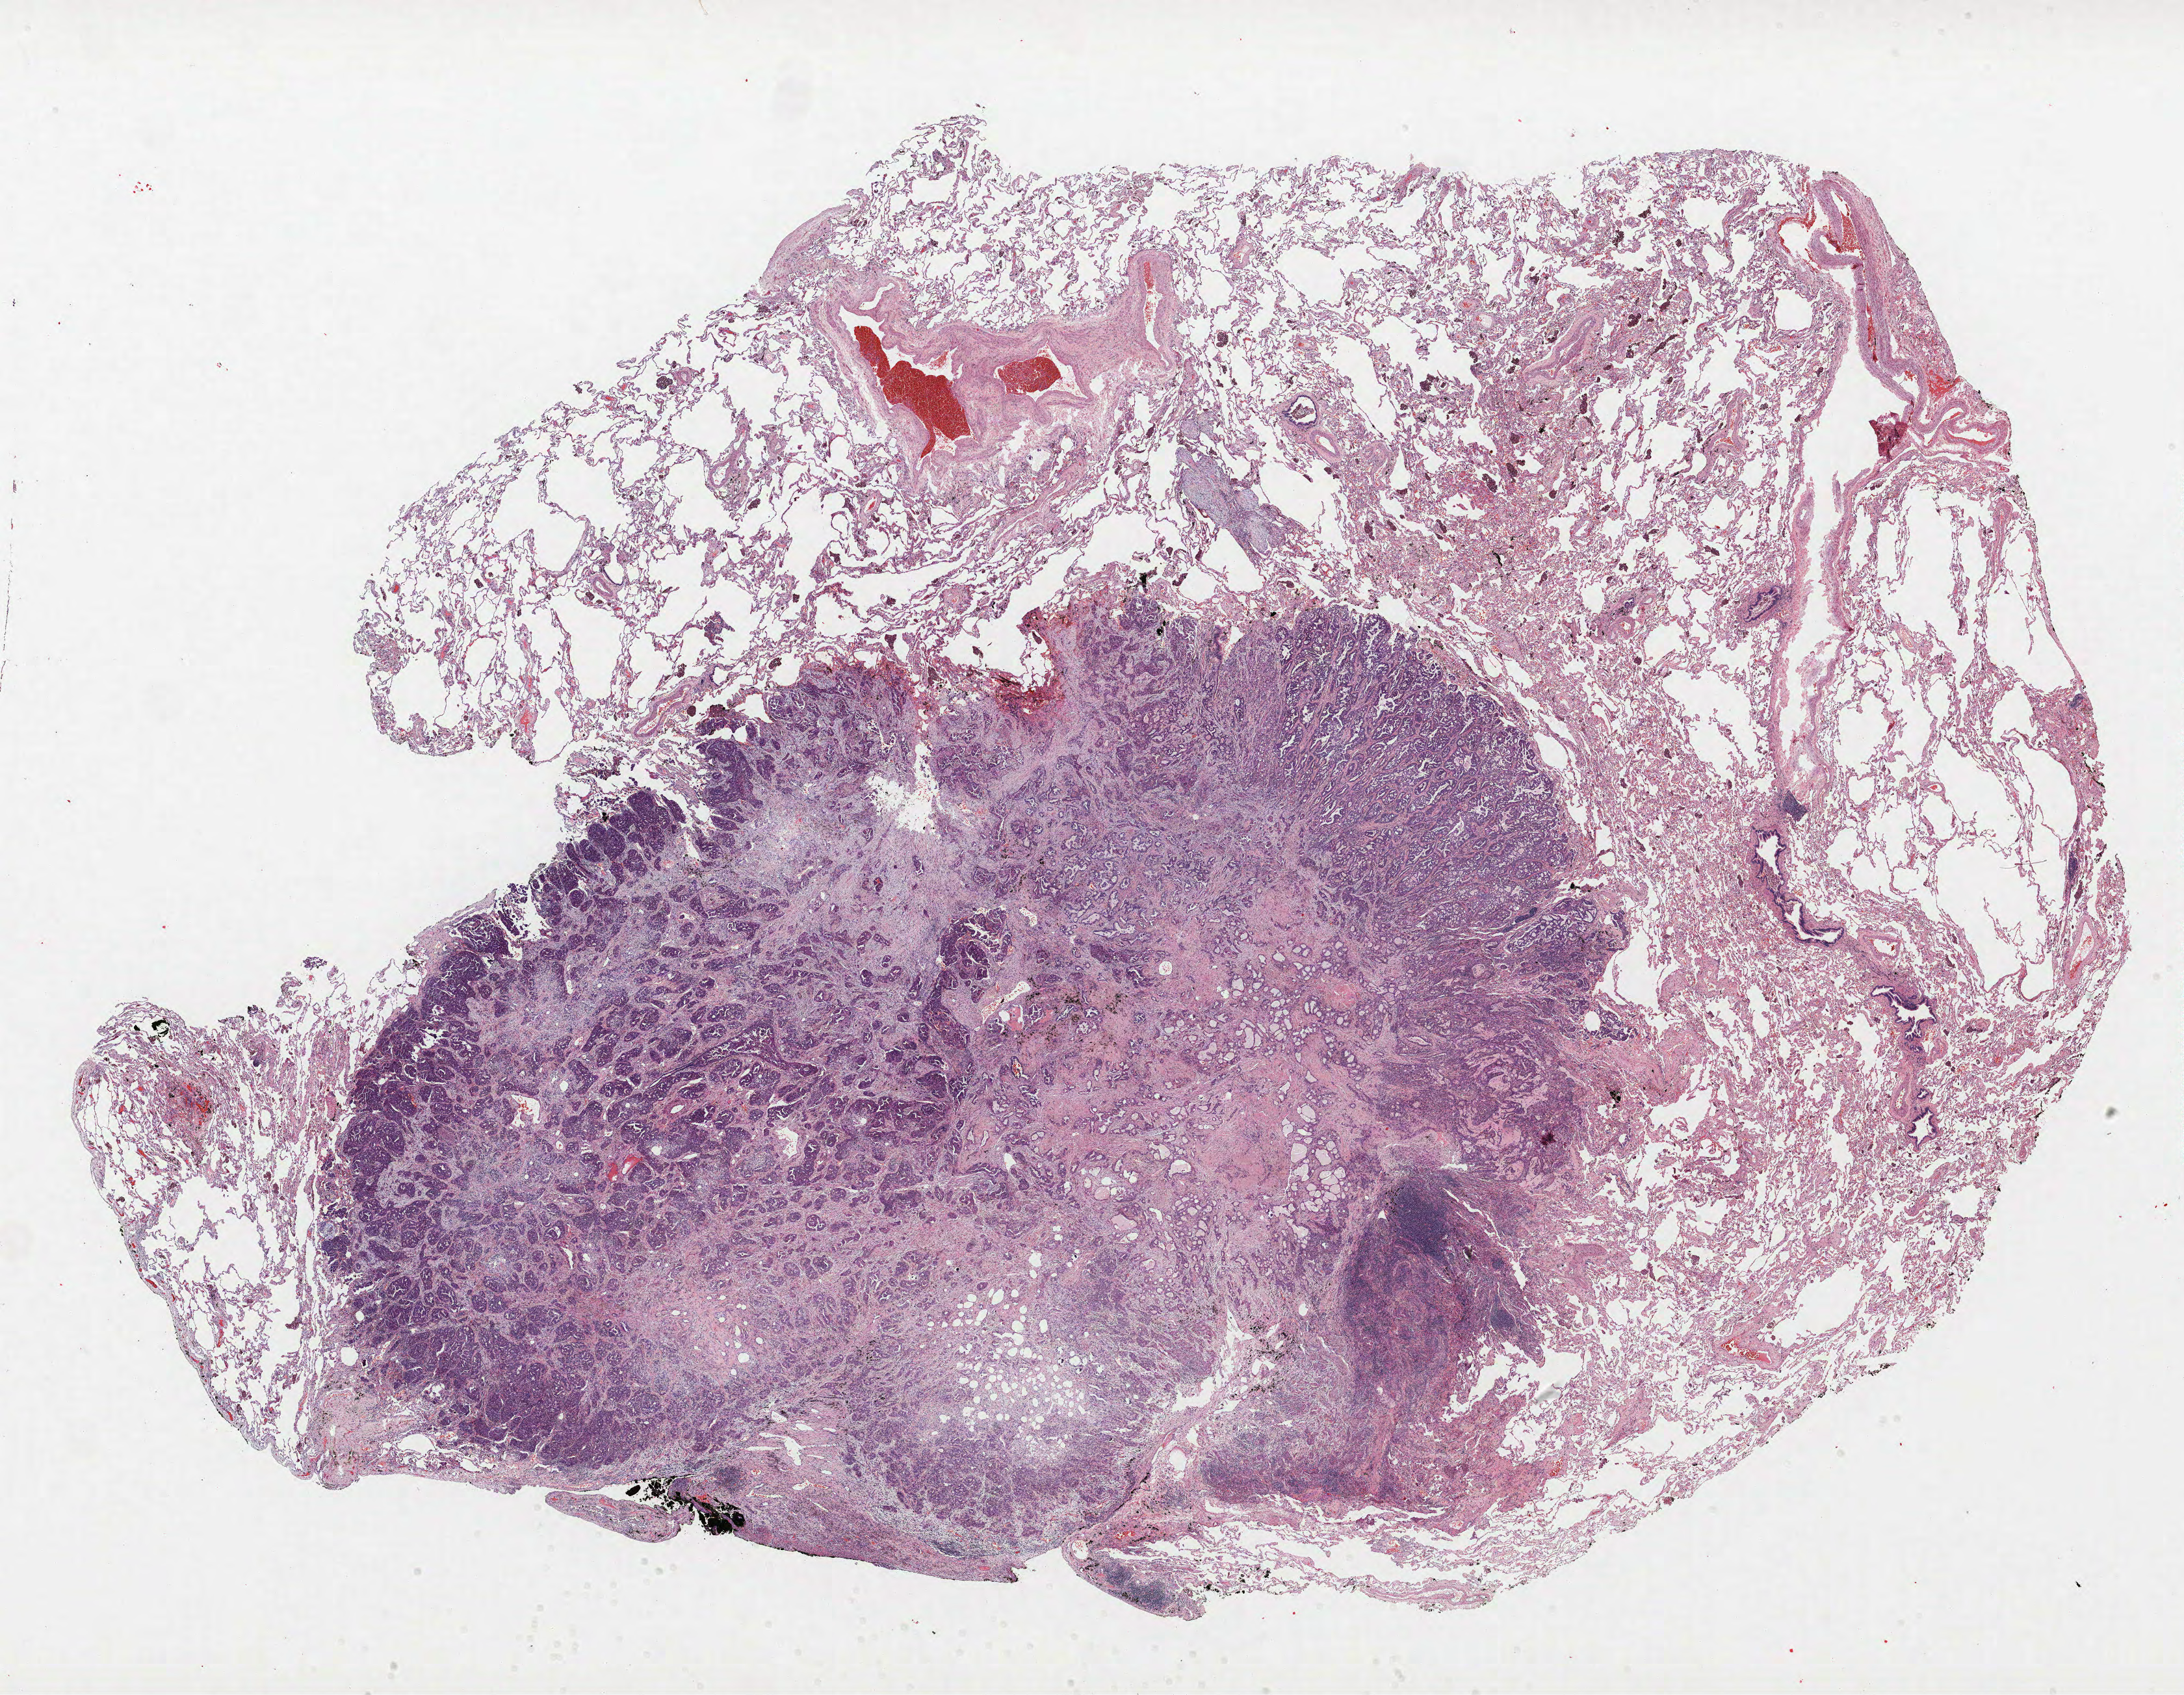
Whole-slide histology image, H&E, a low-resolution overview of the entire scanned area, about 26.9 x 20.9 mm (slide scanned at 40x), FFPE section, lung tissue. Female, age 58 at enrolment. Grade: moderately differentiated (G2).
Stage (AJCC 6th edition): IIA. Participant's lung-cancer diagnosis: Adenocarcinoma, NOS. Tumour size (pathology): 15 mm. Primary tumour location (clinical record): left upper lobe. ICD-O-3 topography: upper lobe of lung (C34.1).